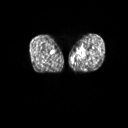
FDG PET of an extremity soft-tissue mass (from a PET/CT study), one axial slice; slice 8 of 267 in the series (ordered by position); 3.27 mm slice thickness; 128 × 128 image matrix, field of view 600 × 600 mm. Male patient, age 59 years. Case-level facts recorded for this patient, not image findings: histological type: pleiomorphic liposarcoma; grade: high; site of the primary tumour: left thigh.
Outlined on this slice (expert contour drawn on MRI and transferred to this co-registered scan by the dataset authors):
- gross tumour volume including surrounding oedema: bounding box [x1, y1, x2, y2] px = [79, 52, 87, 59]